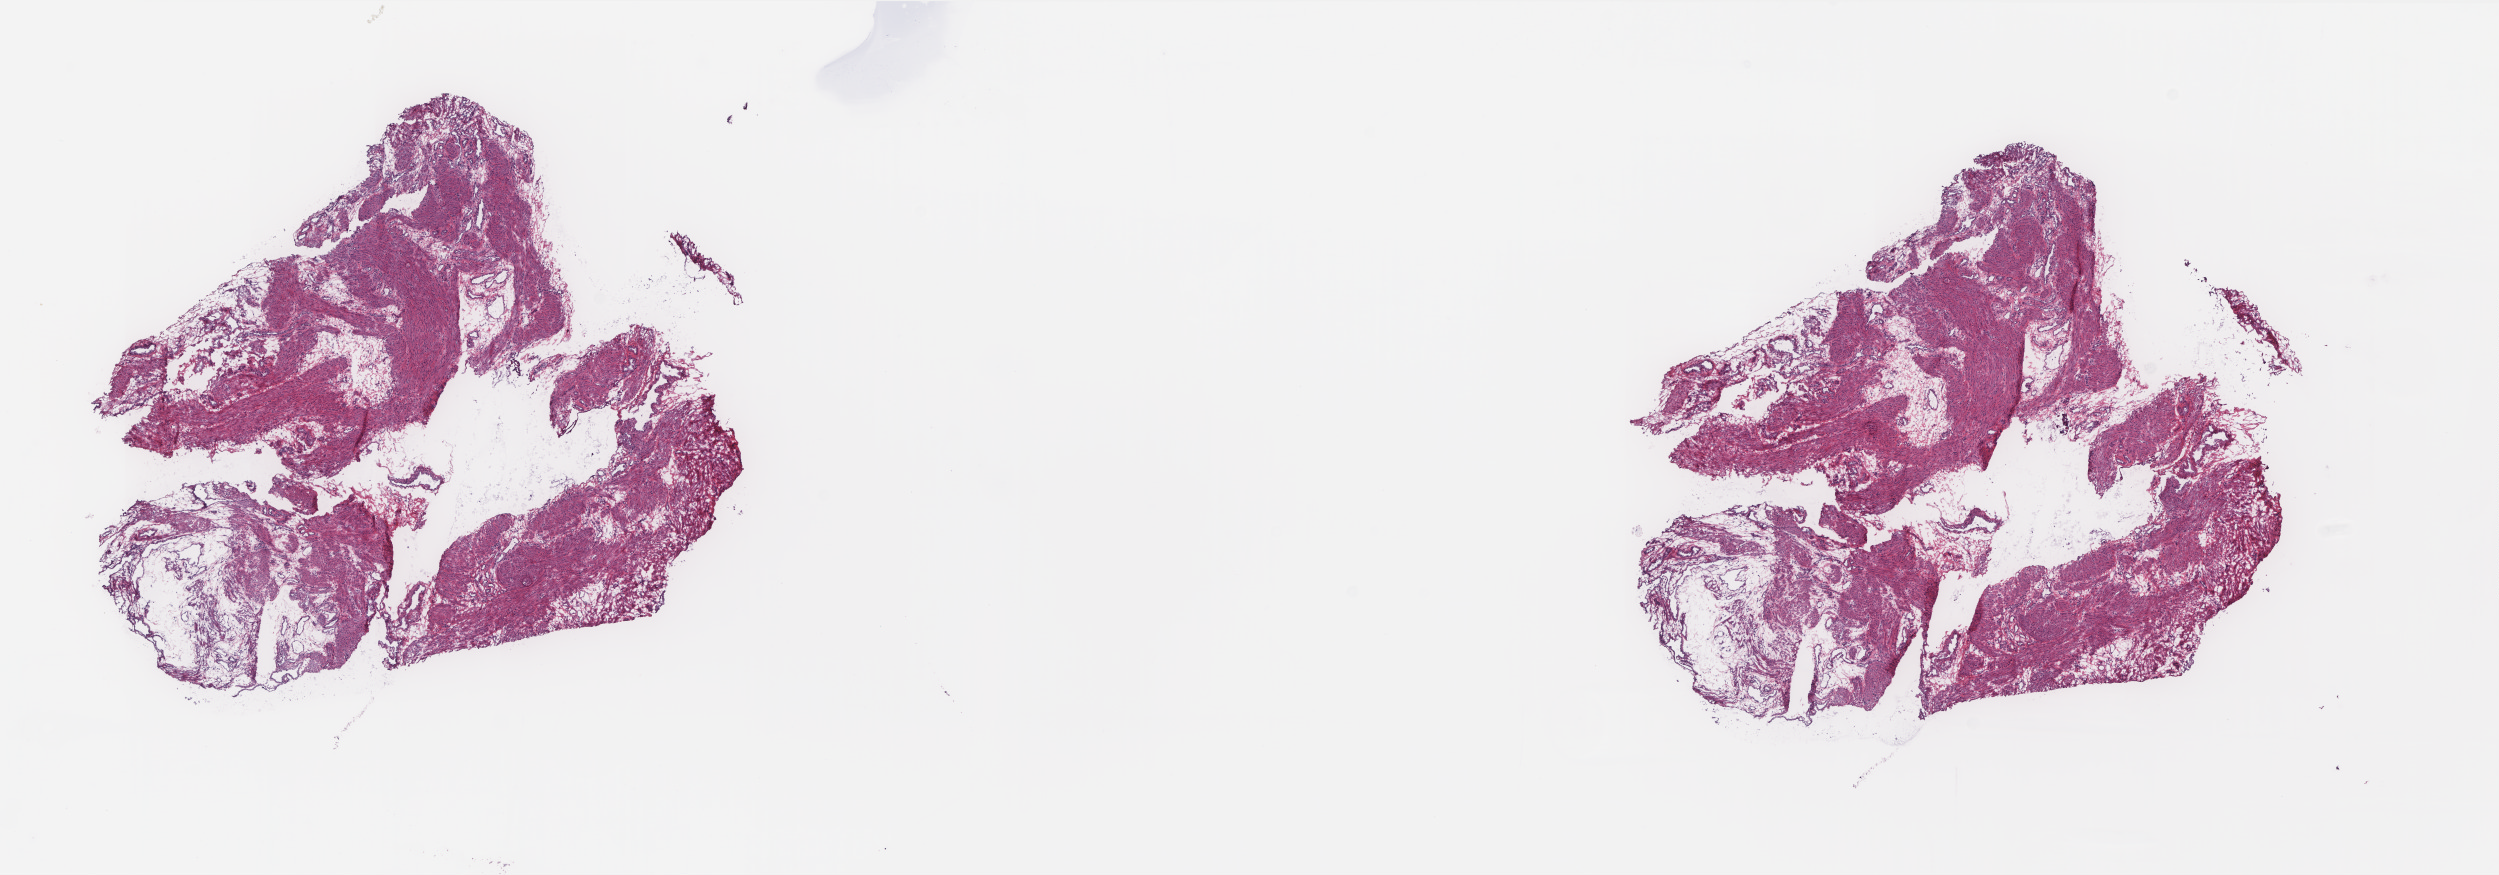
Digitized Hematoxylin and eosin (H&E) stained tissue section (whole slide) — whole scanned area (about 20.0 x 7.0 mm, from a 20x scan) shown as a low-resolution overview; frozen section from the top of the tissue portion; cervix, solid tissue normal (non-tumour tissue) sample. Female, age 40 years at initial diagnosis. Pathologist review of this section (percent, as recorded): tumour cells 0%, tumour nuclei 0%, normal cells 100%, stromal cells 0%, necrosis 0%. Inflammatory infiltration, as recorded: lymphocyte infiltration 1%, monocyte infiltration 0%, neutrophil infiltration 0%.
- this section: solid tissue normal sample (biorepository sample class)
- patient diagnosis: Squamous cell carcinoma, NOS (cervix uteri)